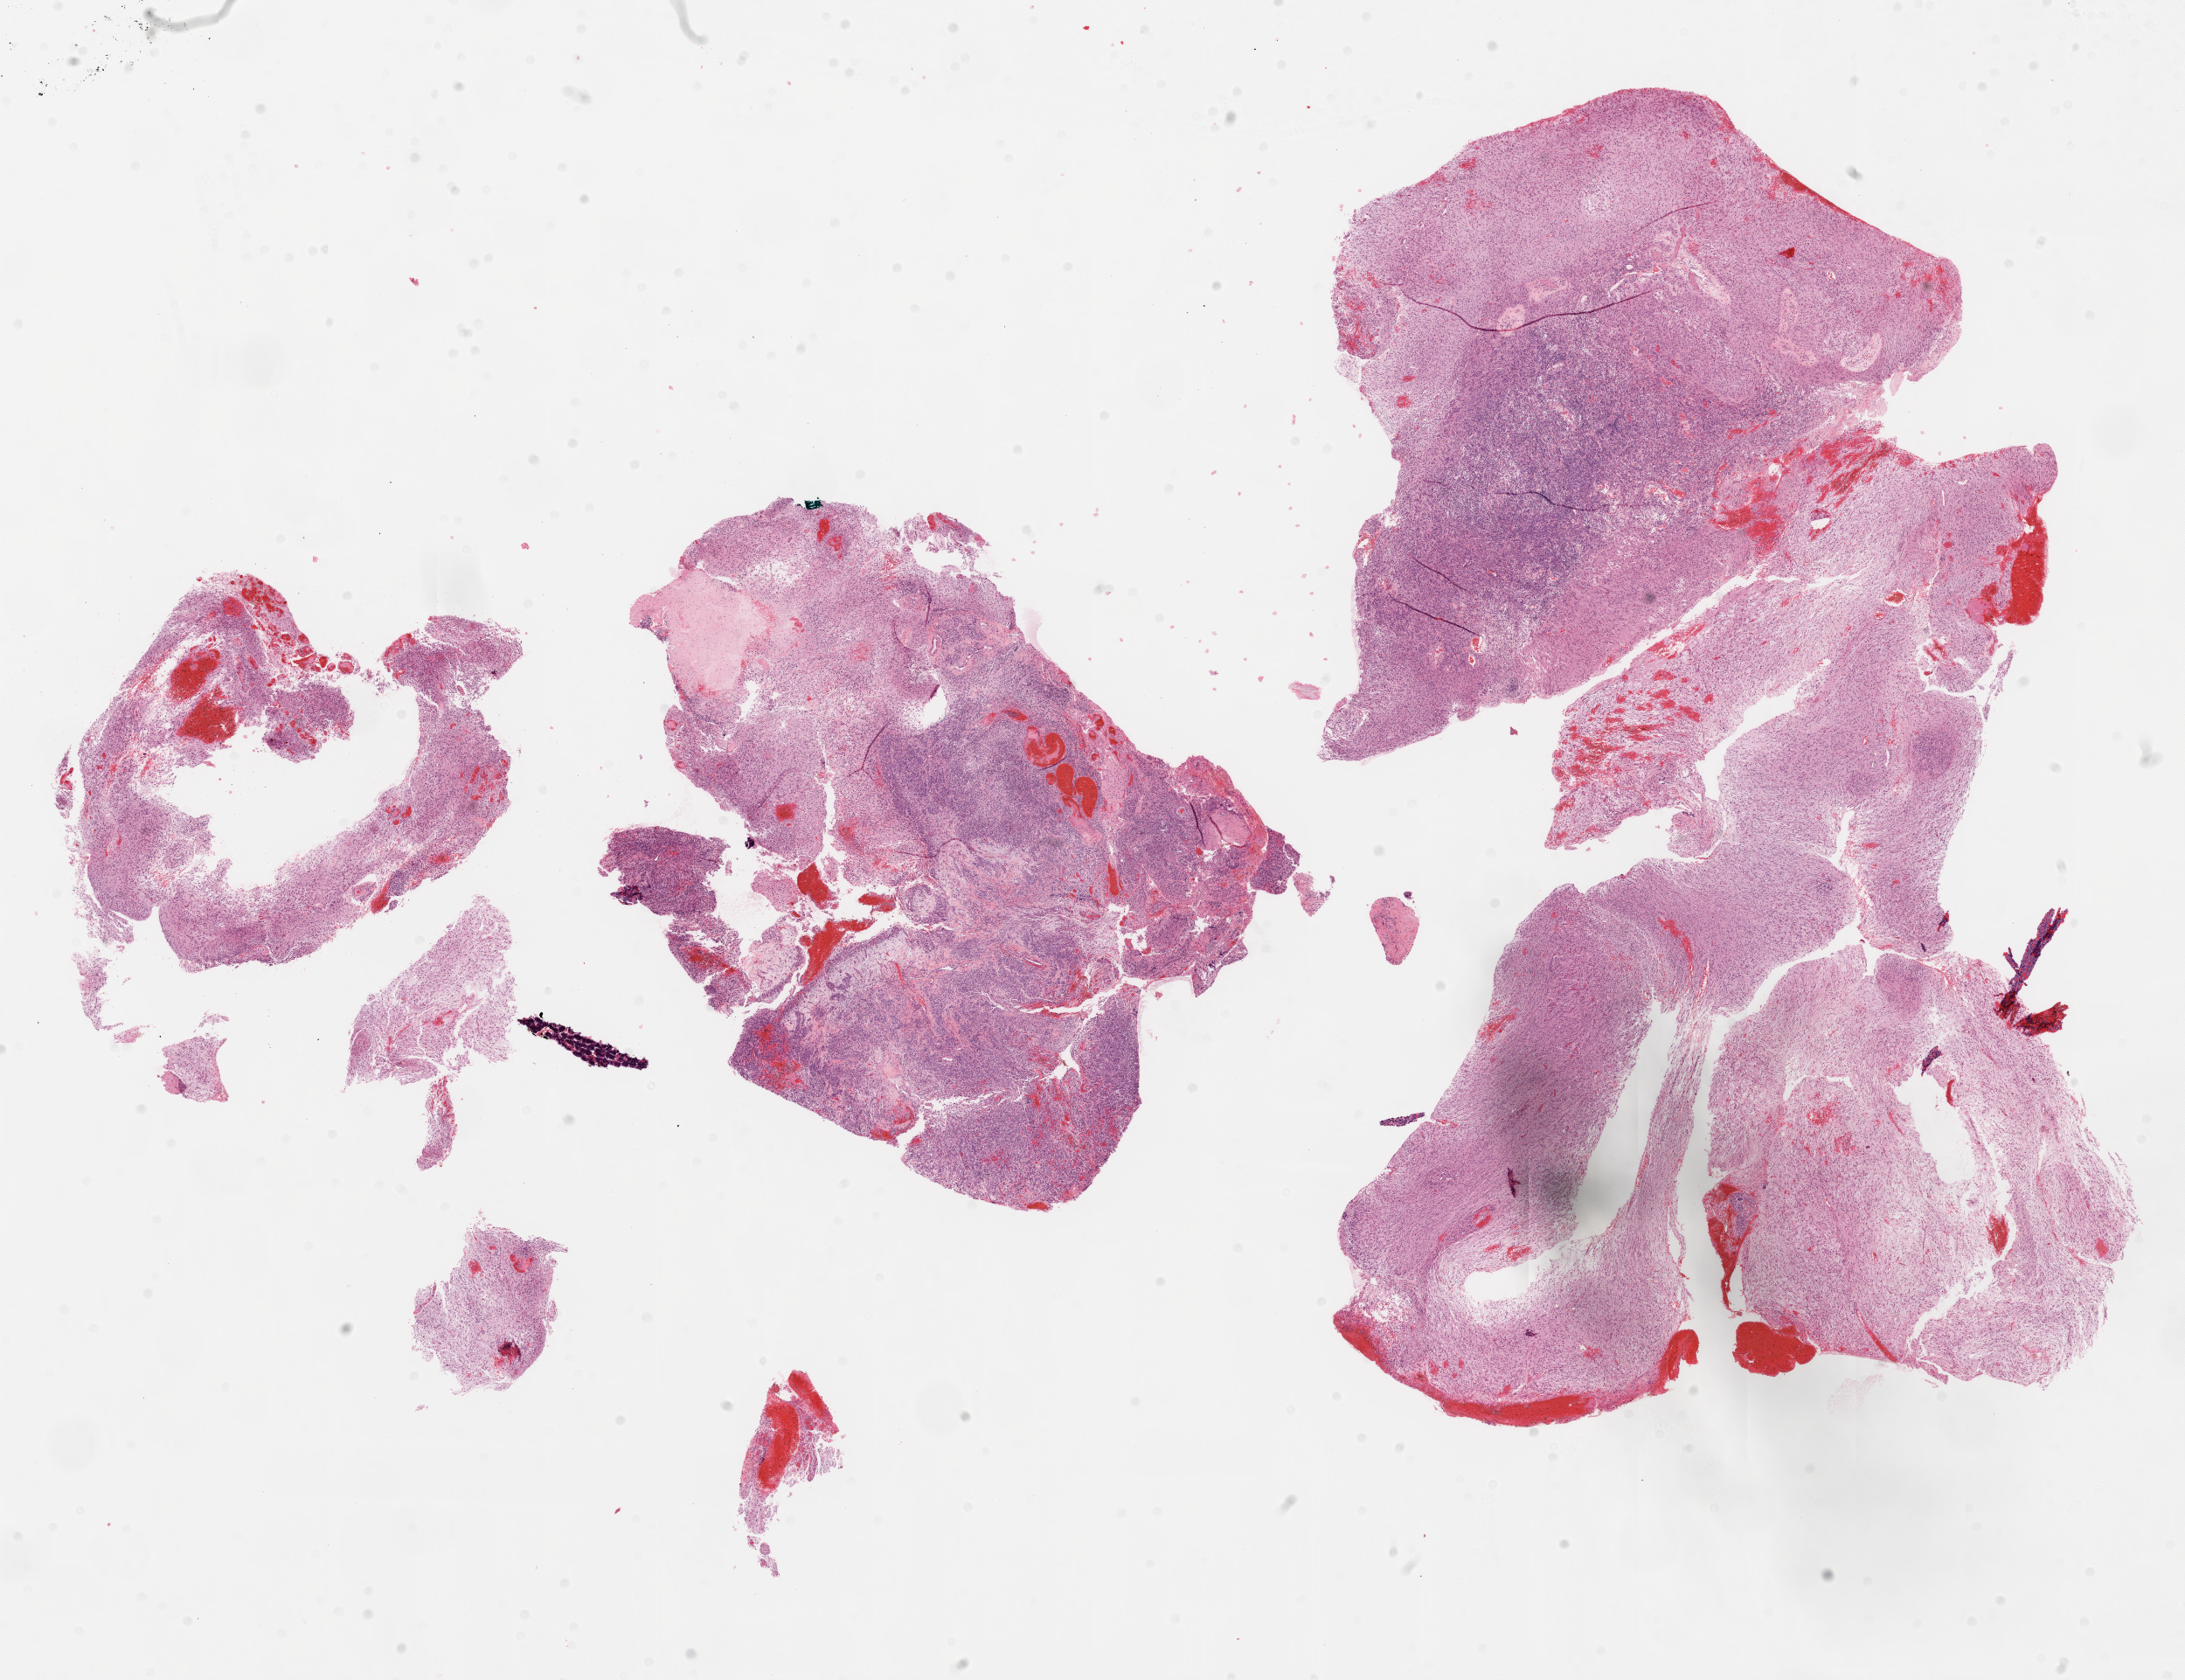
Digitized Hematoxylin and eosin (H&E) stained tissue section (whole slide), whole scanned area (about 20.1 x 15.4 mm, from a 20x scan) shown as a low-resolution overview. FFPE section. Sample: primary tumour, brain. Male, age 70 years at initial diagnosis.
Pathologic diagnosis: Glioblastoma.